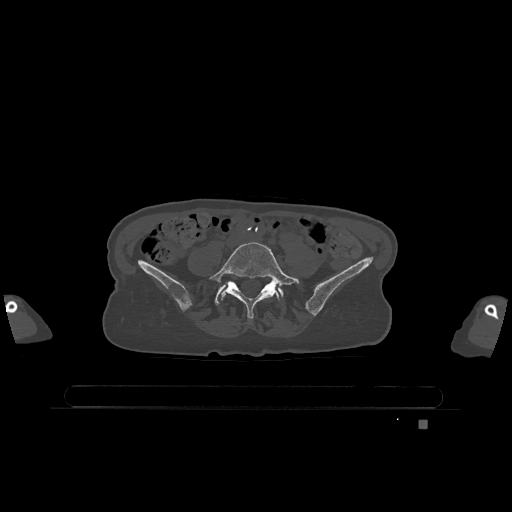
CT including the spine, one axial slice; bone window (W 1800 / L 400 HU); 512 × 512 image matrix, field of view 500 × 500 mm. Female patient, age 74 years. From the clinical record (not read from this slice): primary cancer: lung.
Annotated regions visible in this slice (semi-automatically segmented with operator editing):
- L5 vertebra: box from (x=209, y=242) to (x=300, y=319) px